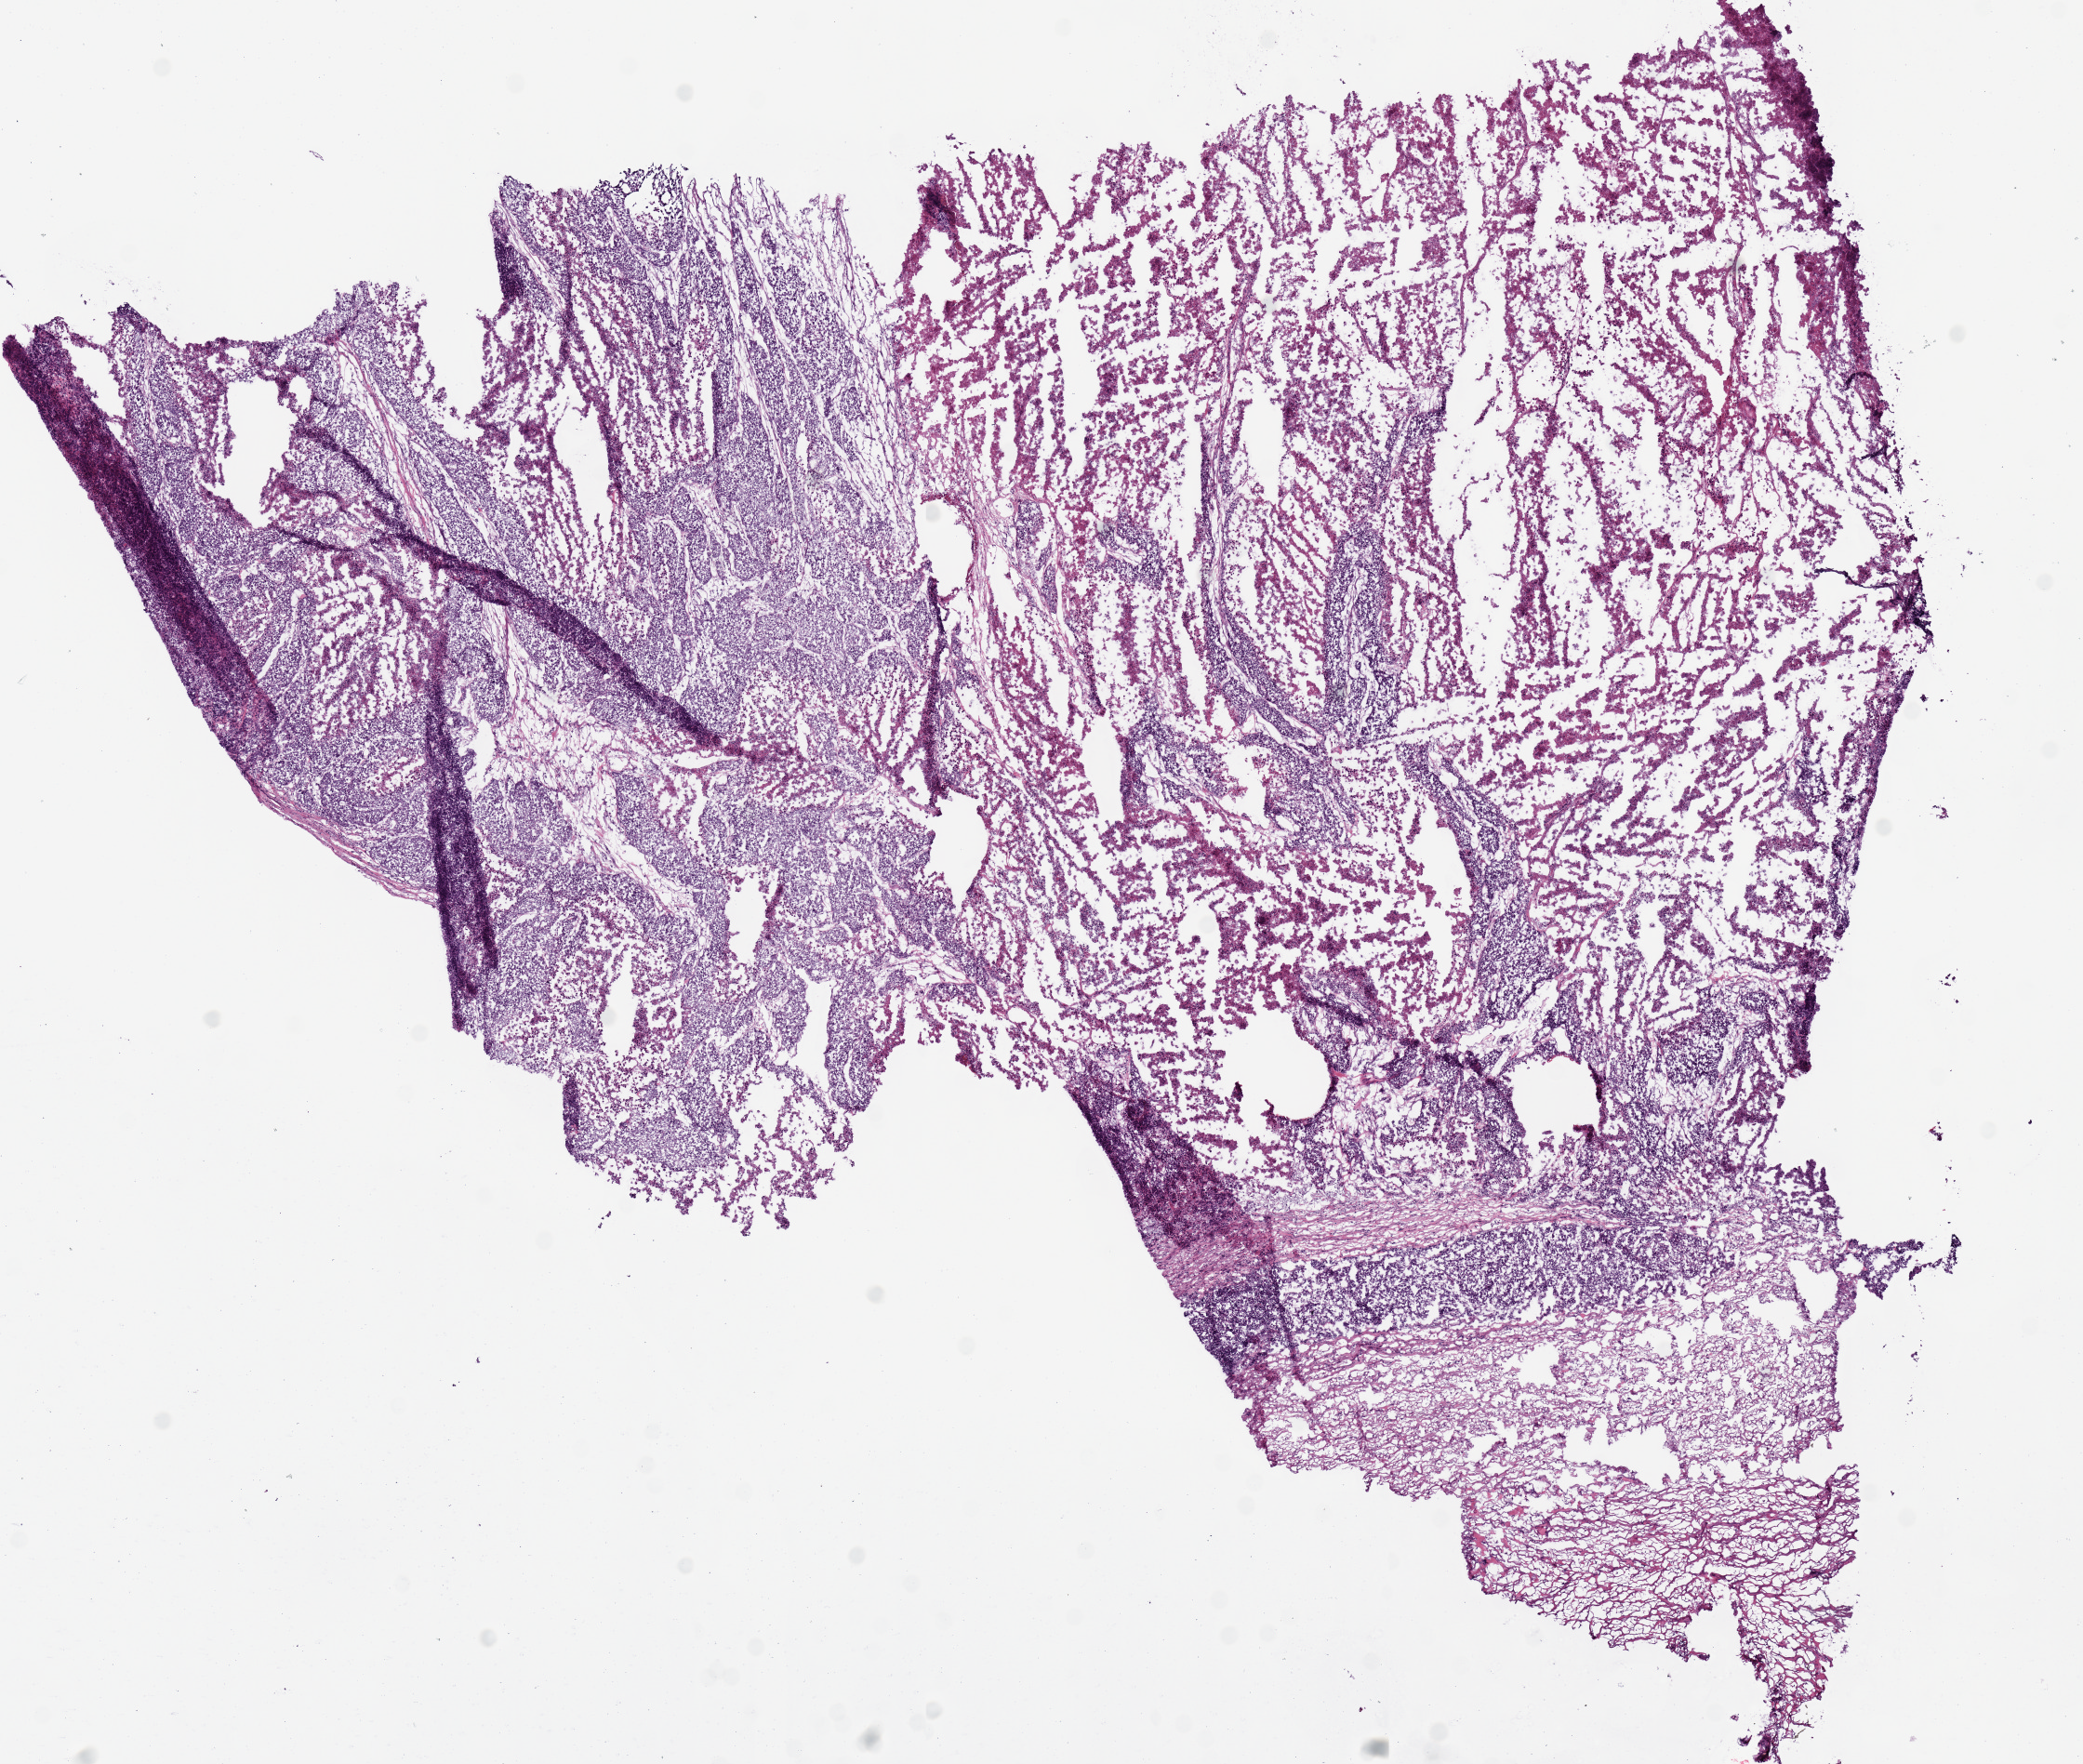
Digitized H&E tissue section (whole slide), shown as a low-resolution overview of the whole scanned area (about 8.9 x 7.5 mm, acquisition: 20x scan). Frozen section. Stomach, primary tumour sample. Patient: female, age at initial diagnosis 70 years. Histologic grade: G3 (poorly differentiated). Slide review estimates, as recorded: tumour nuclei 85%, necrosis 5%.
• AJCC pathologic stage: IIB
• diagnosis: Adenocarcinoma, NOS (body of stomach)